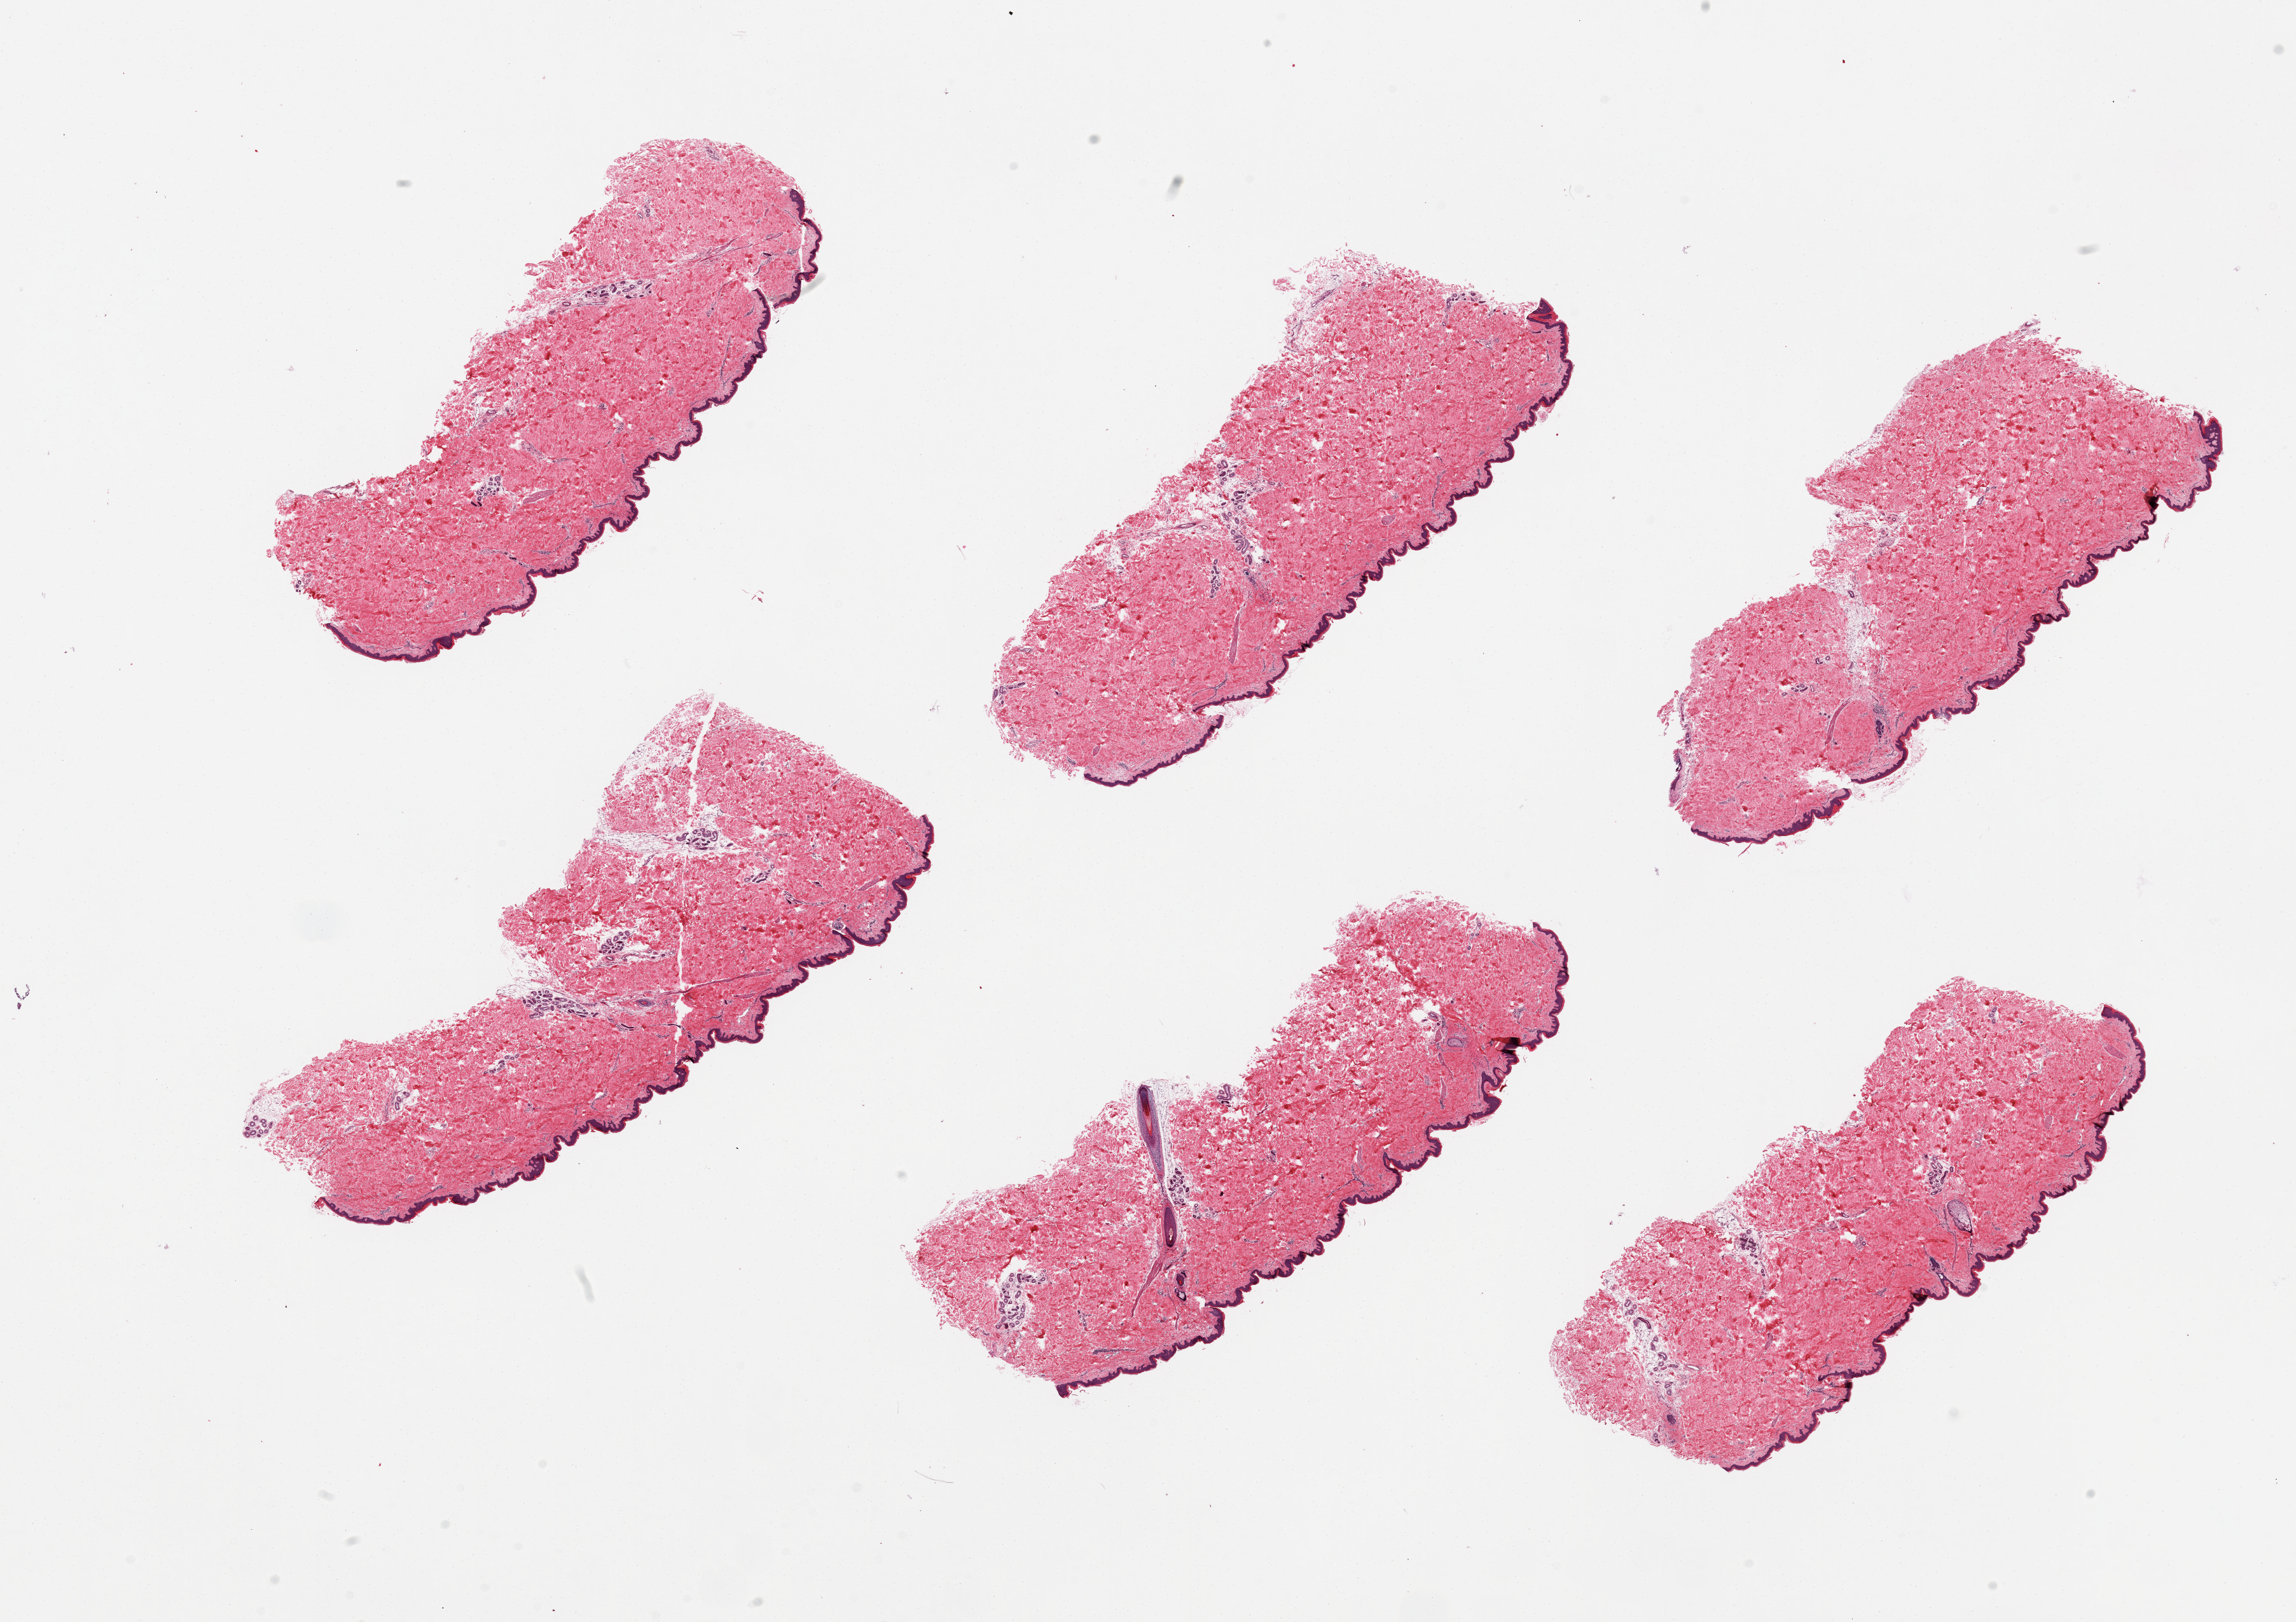
H&E whole-slide image, a low-resolution overview of the entire scanned area, about 28.5 x 20.2 mm; PAXgene-fixed, paraffin-embedded tissue; section of skin of lower leg (target tissue); donor tissue sample.
Review note (as recorded): 6 pieces, minimal subcutaneous fat; squamous epitheliums is ~0.05-0.1mm thick.